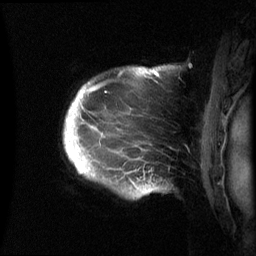
Breast MRI (dynamic contrast-enhanced), one sagittal slice. Position 54 of 60 along the scan axis. Dynamic contrast-enhanced series, image 2 of 3 at this slice position (ordered by acquisition). 1.5 T. TE 4.2 ms, TR 8.4 ms. 2.4 mm slice thickness. 256 × 256 image matrix. Female patient, age 48 years.
Structures marked on this image (semi-automatically segmented with operator editing):
- analysis volume of interest (the breast-tissue region the enhancement analysis was run in; not a lesion): bounding box <64,67,160,198> (left, top, right, bottom; pixels)
- tumour enhancement mask (voxels above the 70 % enhancement threshold inside the analysis volume of interest): <66,70,157,166>